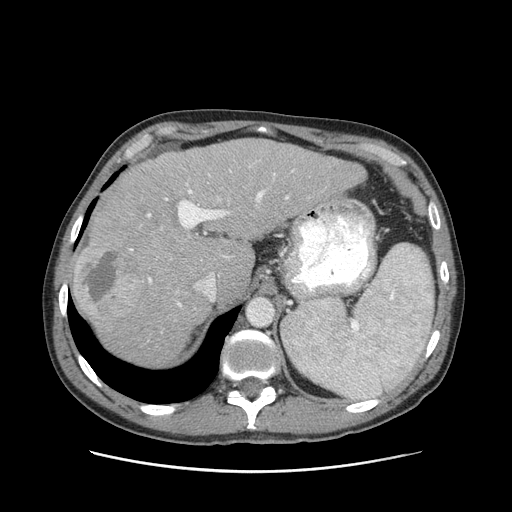
Contrast-enhanced abdominal CT (liver protocol), one axial slice; position 70 of 93 along the scan axis; soft-tissue window (W 400 / L 40 HU); 2.5 mm slice thickness; 512 × 512 image matrix, field of view 380 × 380 mm. From the clinical record (not read from this slice): diagnosis: hepatocellular carcinoma (patient treated with transarterial chemoembolisation; whether this scan precedes or follows treatment is not stated here); TNM stage (as recorded): Stage-II; Child-Pugh class: A.
Structures marked on this image (semi-automatically segmented with operator editing):
- liver parenchyma outside the tumour (the mass and vessels are separate outlines, so this box may not span the whole liver): box from (x=72, y=138) to (x=366, y=366) px
- mass: (x=74, y=244)–(x=142, y=320)
- liver vessels: (x=77, y=170)–(x=294, y=307)